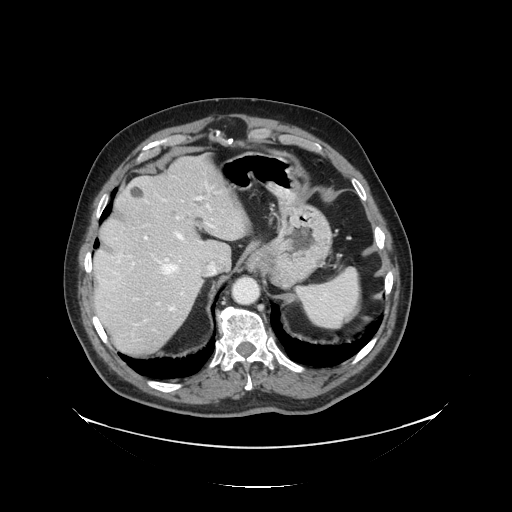
Contrast-enhanced abdominal CT, one axial slice. Position 104 of 138 along the scan axis. 120 kVp. Intravenous contrast given. Soft-tissue window (W 400 / L 40 HU). 2.5 mm slice thickness. 512 × 512 image matrix, field of view 497 × 497 mm. Male patient, age 77 years. Case-level facts recorded for this patient, not image findings: diagnosis: colorectal cancer liver metastases, imaged before liver resection; multiple liver metastases: no; largest metastasis: 1.5 cm; chemotherapy before resection: no.
Annotated regions visible in this slice (manually delineated by an expert):
- hepatic veins: box from (x=156, y=204) to (x=213, y=311) px
- liver: (x=94, y=157)–(x=249, y=357)
- planned liver remnant (the part of the liver to remain after resection): (x=93, y=158)–(x=249, y=290)
- portal vein (with intrahepatic branches): (x=132, y=188)–(x=217, y=322)
- liver metastasis: (x=196, y=216)–(x=204, y=224)
- liver metastasis: (x=130, y=186)–(x=143, y=198)